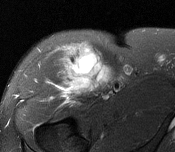
MRI of an extremity soft-tissue mass, one axial slice; slice 109 of 116 in the series (ordered by position); T2-weighted fat-saturated; MR volume resampled by the dataset authors to the PET/CT grid (not the native acquisition matrix); 3.27 mm slice thickness; 175 × 152 image matrix. Male patient. From the clinical record (not read from this slice): histological type: pleiomorphic leiomyosarcoma; grade: intermediate; site of the primary tumour: right thigh.
Structures marked on this image (expert contour drawn on MRI and transferred to this co-registered scan by the dataset authors):
- gross tumour volume including surrounding oedema: bounding box (x1, y1, x2, y2) in pixels: (63, 47, 109, 94)
- gross tumour volume (mass): (70, 56, 107, 93)